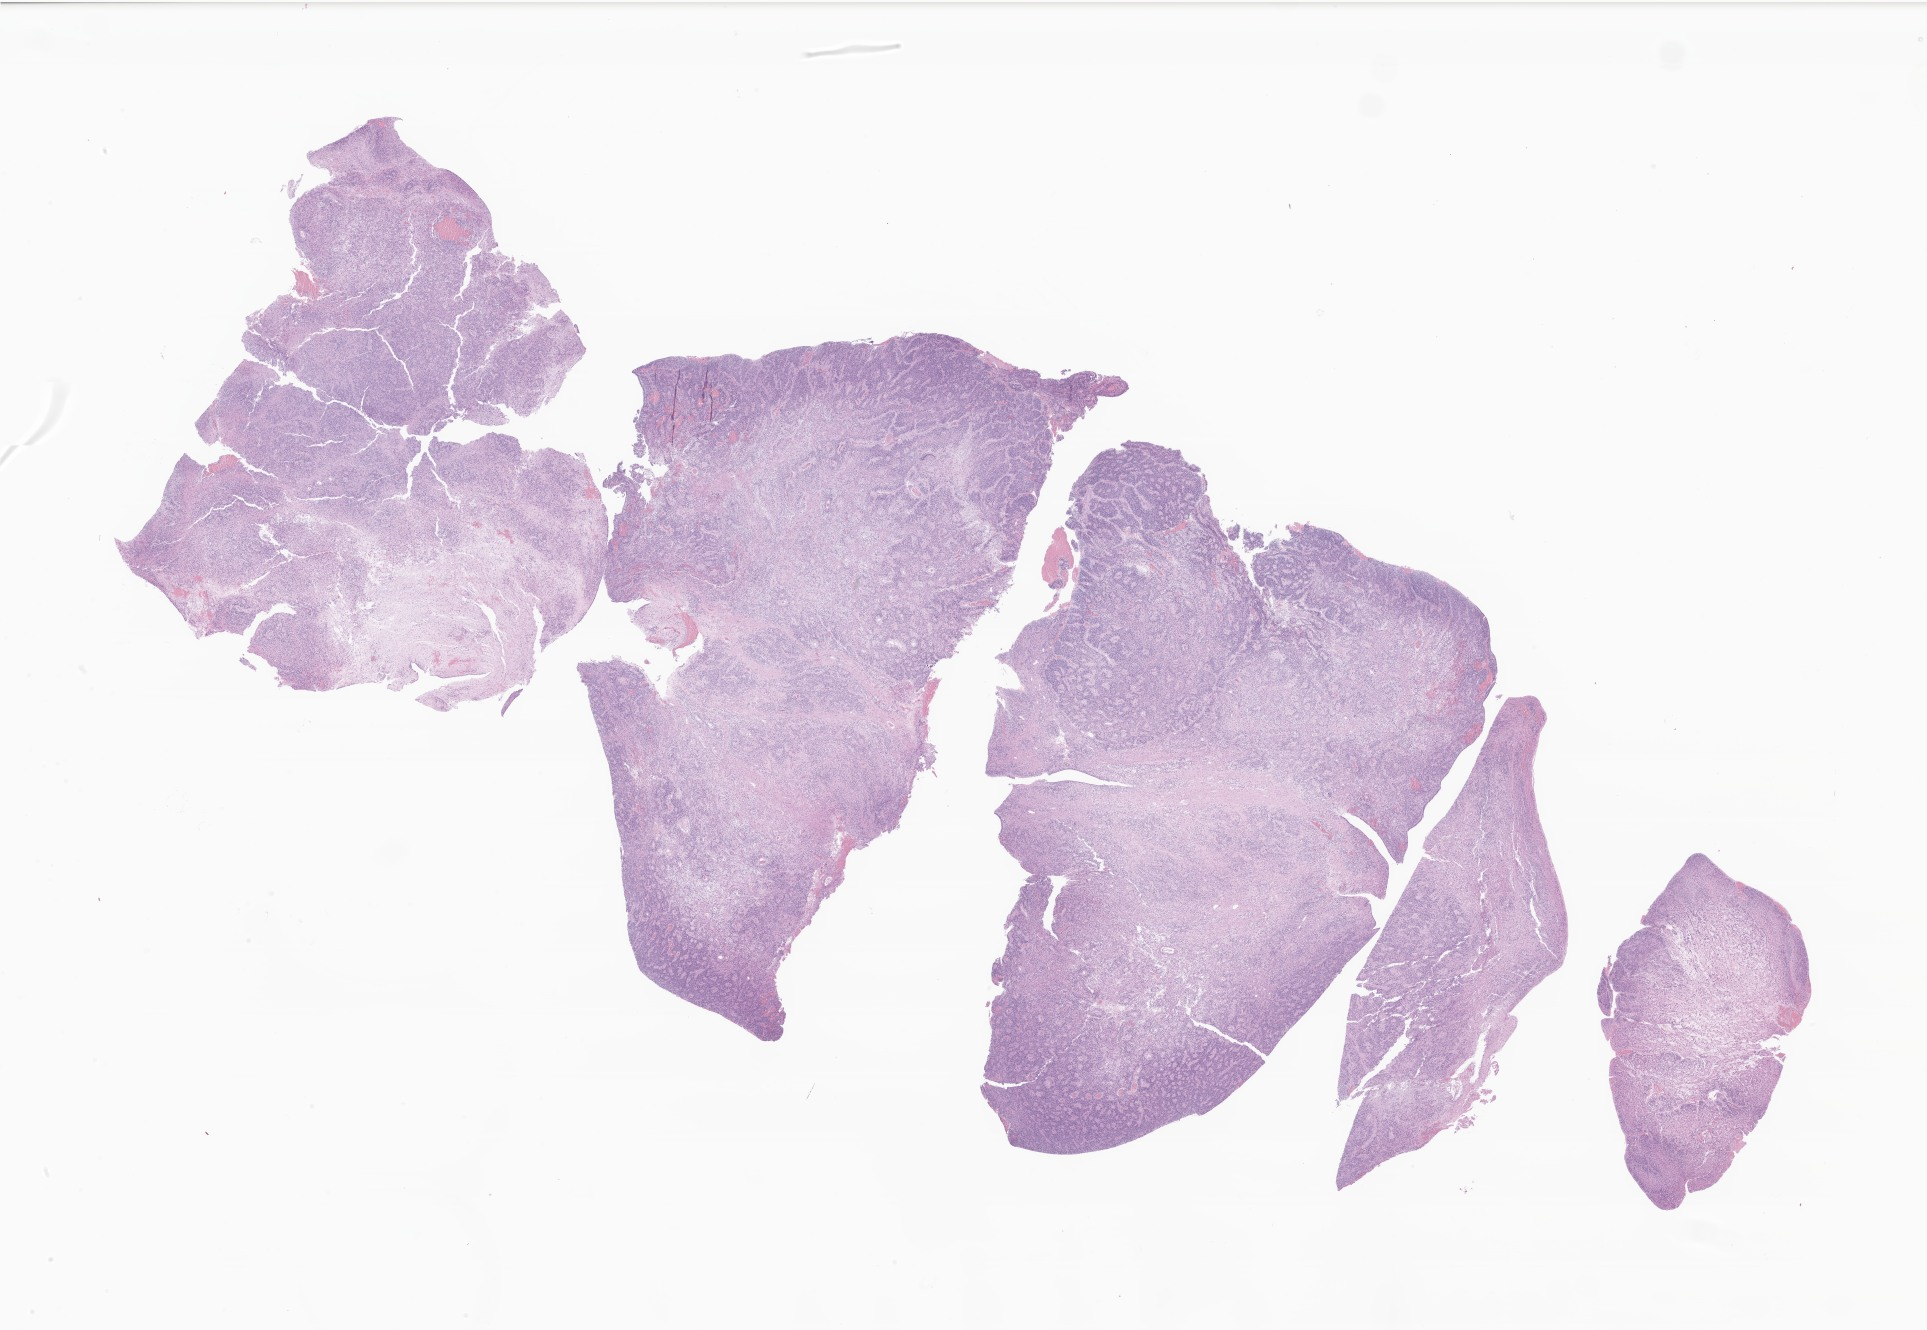
H&E whole-slide image of tumor tissue from the brain — a low-resolution overview of the entire scanned area, about 32.5 x 22.4 mm; FFPE section. Patient: male, age 467 days.
- recorded diagnosis: Ependymoma, NOS